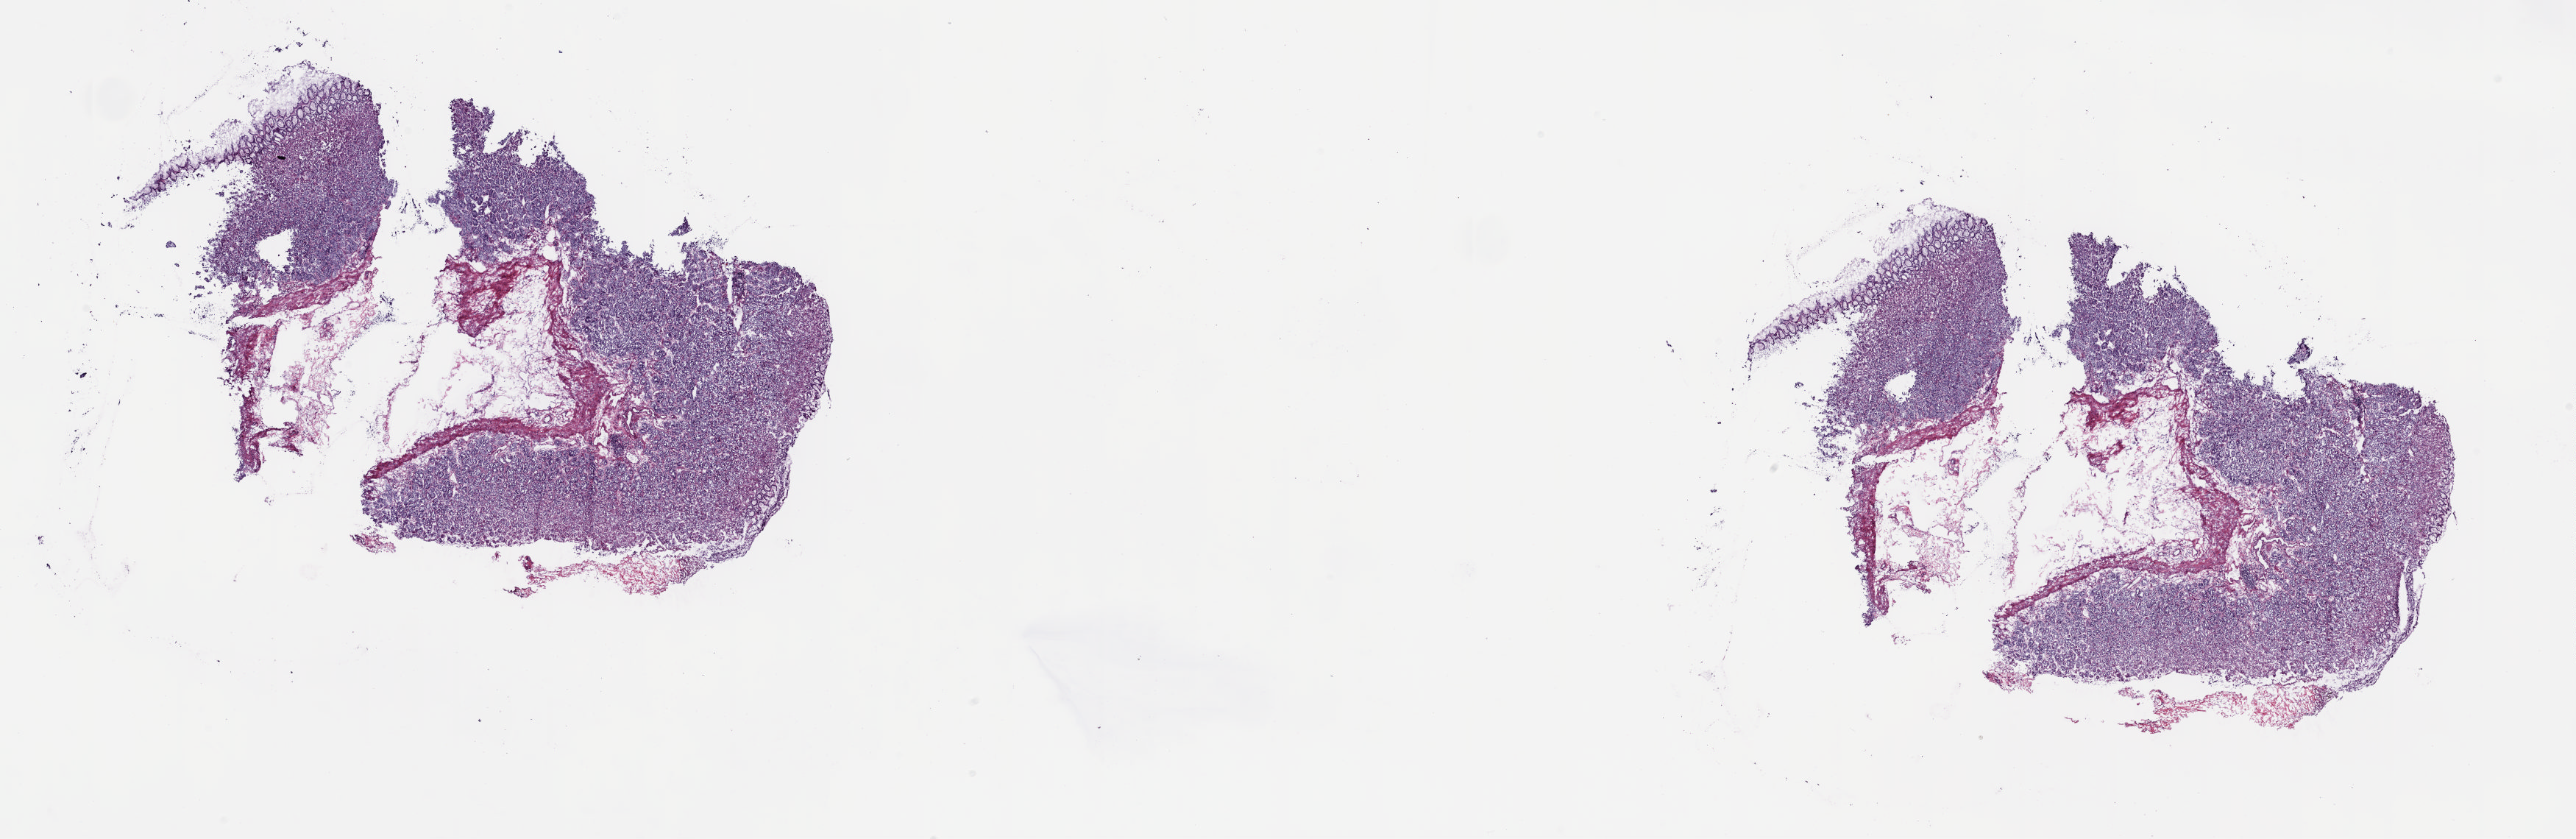
Whole-slide histology image, H&E — low-resolution overview of the scanned area, about 27.8 x 9.0 mm. Frozen section from the top of the tissue portion. Esophagus, solid tissue normal (non-tumour tissue) sample. Male patient; age at initial diagnosis 43 years. Slide review estimates, as recorded: tumour cells 0%, tumour nuclei 0%.
This section: solid tissue normal sample (biorepository sample class). Patient diagnosis: Adenocarcinoma, NOS (lower third of esophagus).